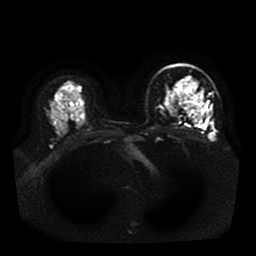
Breast MRI, one axial slice. Slice 28 of 41 in the series (ordered by position). Diffusion-weighted series; image 2 of 4 stored at this slice position (different b-values; order by instance number). 1.5 T. 256 × 256 image matrix, field of view 330 × 330 mm. Female patient.
Outlined on this slice (expert manual segmentation):
- tumour on diffusion-weighted imaging: bounding box <199,105,204,121> (left, top, right, bottom; pixels)